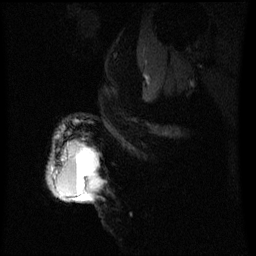
Breast MRI (dynamic contrast-enhanced), one sagittal slice. Slice 46 of 60 in the series (ordered by position). Dynamic contrast-enhanced series, image 2 of 3 at this slice position (ordered by acquisition). 1.5 T. TE 4.2 ms, TR 8 ms. 2.2 mm slice thickness. 256 × 256 image matrix. Patient: female, 50 years.
Annotated regions visible in this slice (semi-automatic segmentation, software-assisted and operator-edited):
- analysis volume of interest (the breast-tissue region the enhancement analysis was run in; not a lesion): bounding box [x1, y1, x2, y2] px = [50, 138, 100, 203]
- tumour enhancement mask (voxels above the 70 % enhancement threshold inside the analysis volume of interest): [52, 150, 100, 203]